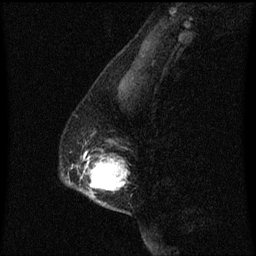
Breast MRI (dynamic contrast-enhanced), one sagittal slice. Dynamic contrast-enhanced series, image 2 of 3 at this slice position (ordered by acquisition). 1.5 T. TE 4.2 ms, TR 8.4 ms. 2 mm slice thickness. 256 × 256 image matrix, field of view 200 × 200 mm. Female patient, age 40 years. From the clinical record (not read from this slice): setting: breast cancer imaged before/during neoadjuvant chemotherapy; receptor status: triple-negative.
Outlined on this slice (semi-automatically segmented with operator editing):
- analysis volume of interest (the breast-tissue region the enhancement analysis was run in; not a lesion): bounding box <64,140,127,213> (left, top, right, bottom; pixels)
- tumour enhancement mask (voxels above the 70 % enhancement threshold inside the analysis volume of interest): <90,158,127,197>